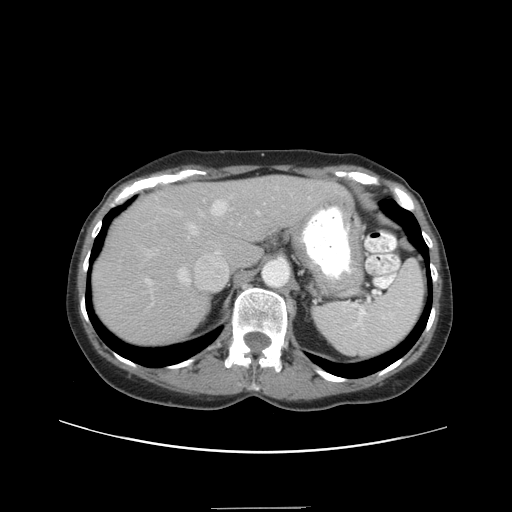
Contrast-enhanced abdominal CT, one axial slice. Slice 28 of 38 in the series (ordered by position). Soft-tissue window (W 400 / L 40 HU). 5 mm slice thickness. 512 × 512 image matrix, field of view 388 × 388 mm. Female patient, age 64 years. Case-level facts recorded for this patient, not image findings: diagnosis: colorectal cancer liver metastases, imaged before liver resection; multiple liver metastases: no; largest metastasis: 3.8 cm; chemotherapy before resection: yes.
Outlined on this slice (manually delineated by an expert):
- hepatic veins: bounding box <150,200,227,293> (left, top, right, bottom; pixels)
- liver: <97,177,339,345>
- planned liver remnant (the part of the liver to remain after resection): <141,177,339,266>
- portal vein (with intrahepatic branches): <145,211,259,285>